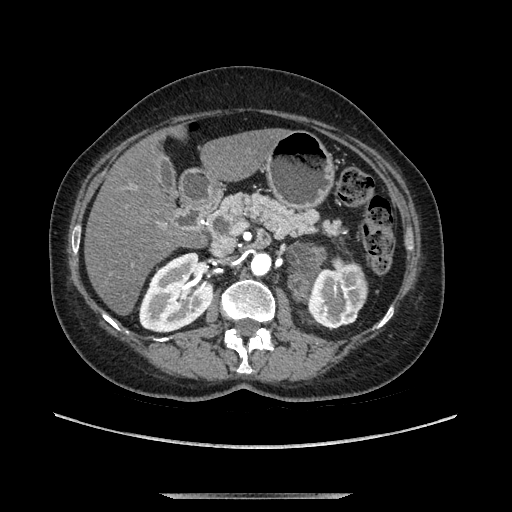
Contrast-enhanced abdominal CT, one axial slice. Slice 57 of 169 in the series (ordered by position). Soft-tissue window (W 400 / L 40 HU). 1.25 mm slice thickness. 512 × 512 image matrix. Female patient. Case-level facts recorded for this patient, not image findings: diagnosis: adrenocortical carcinoma; tumour side: left adrenal; tumour size at pathology: 9 cm; Ki-67 index: 2 %; stage (as recorded): 3.
Structures marked on this image (semi-automatic segmentation, software-assisted and operator-edited):
- mass: bounding box [x1, y1, x2, y2] px = [288, 246, 321, 301]